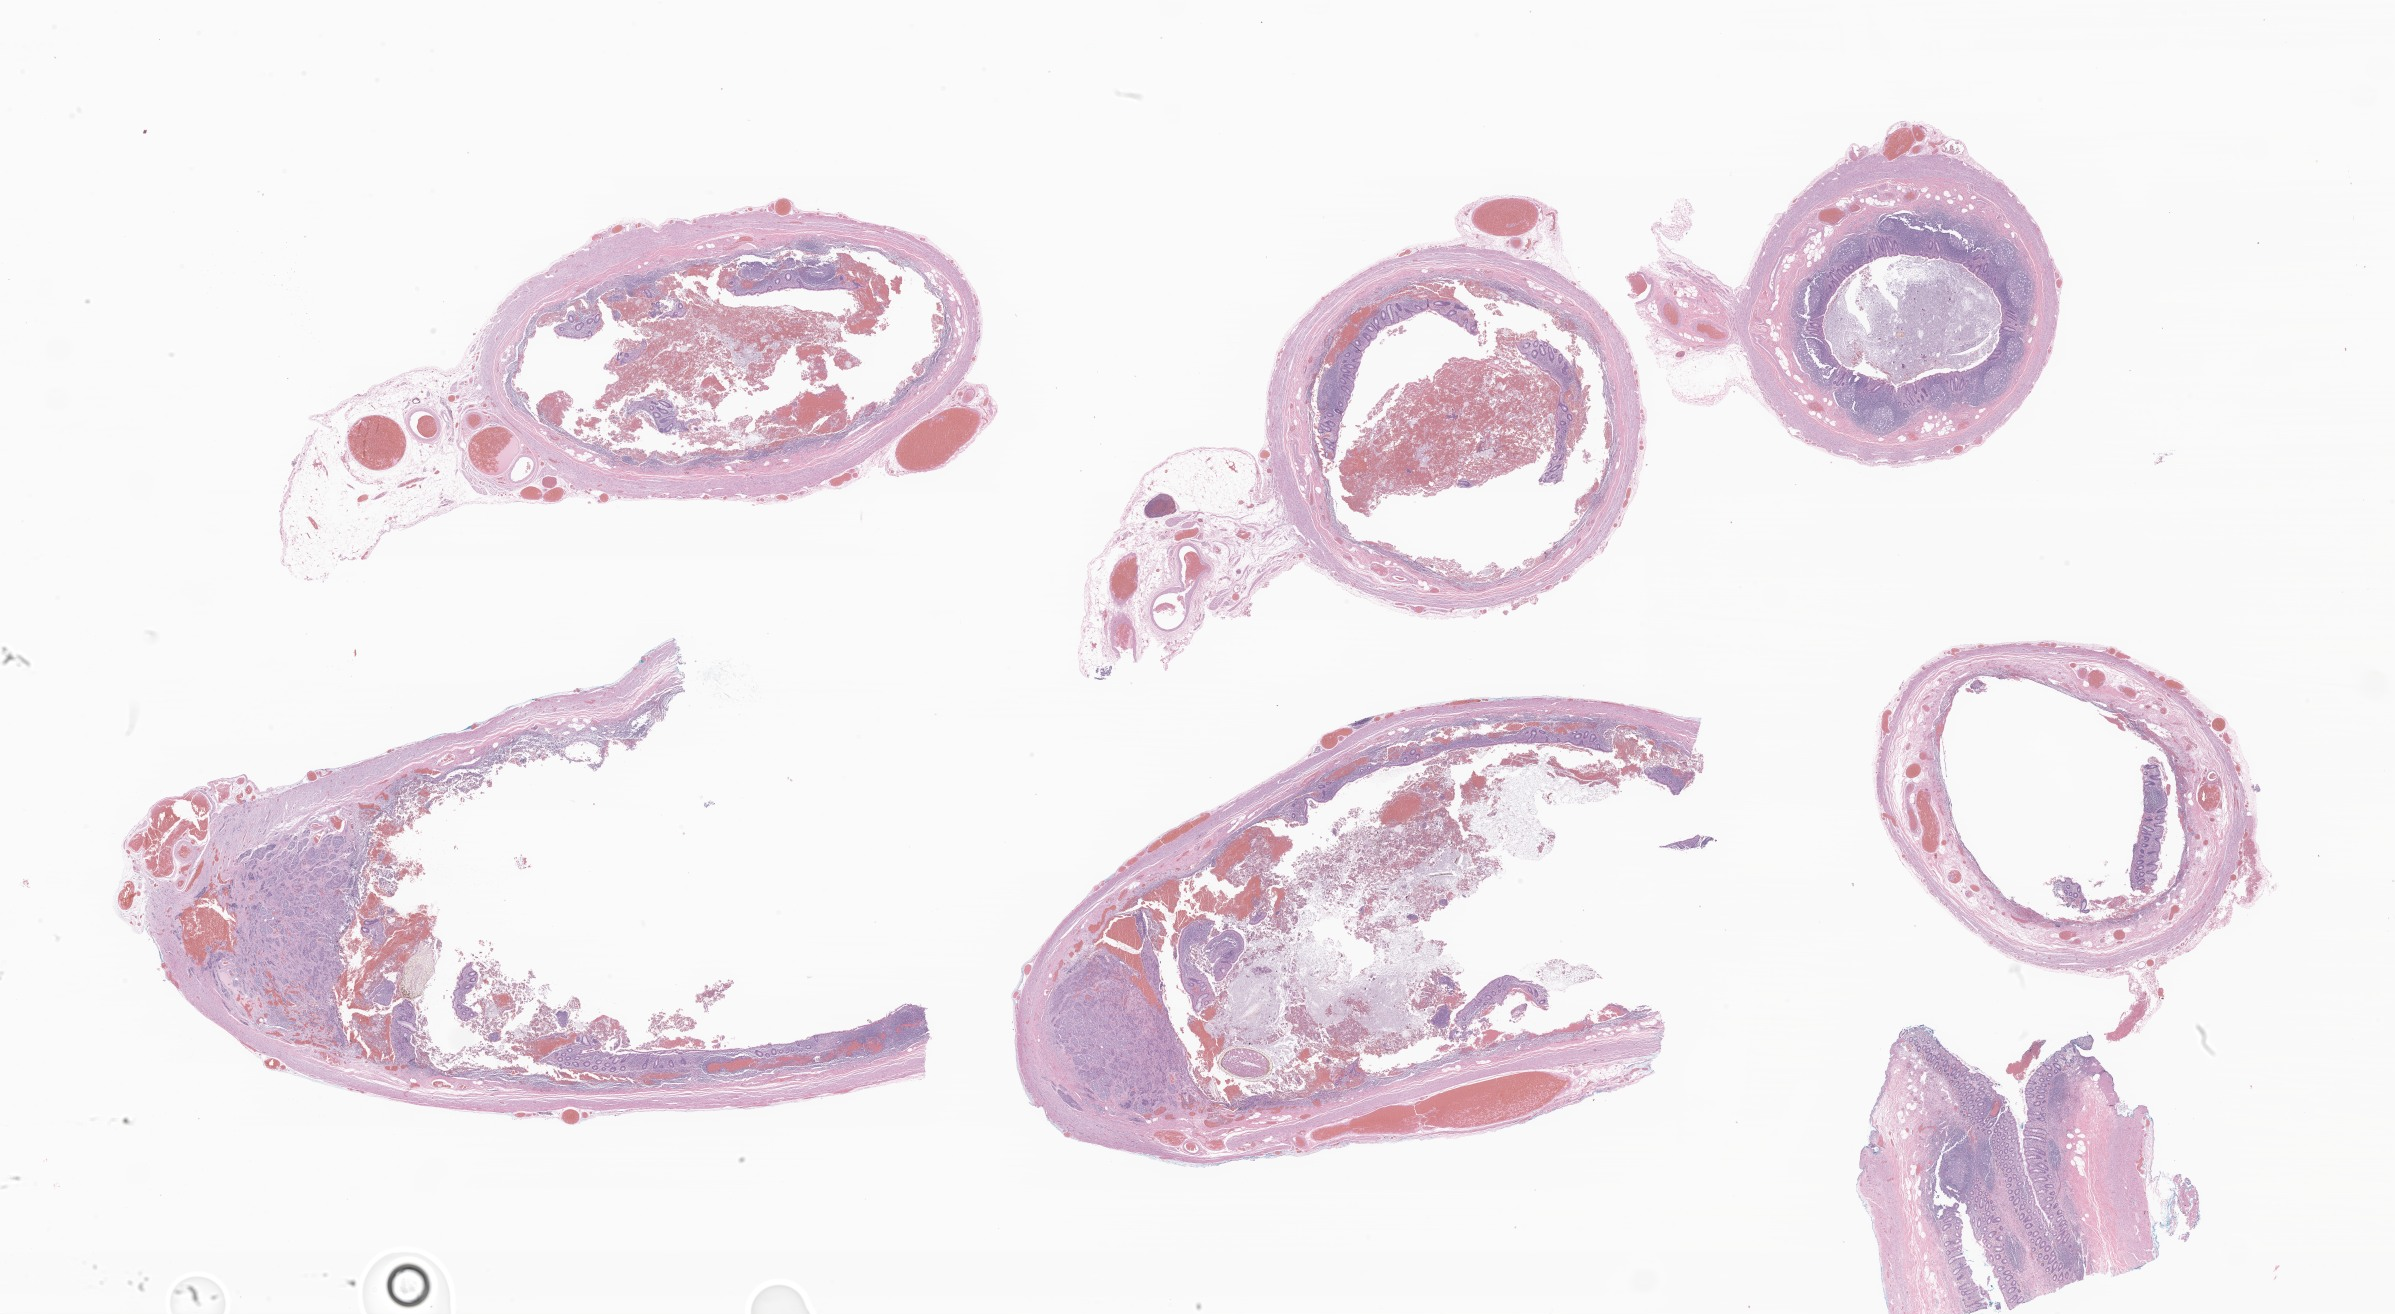
Digitized H&E-stained section of tumor tissue from the appendix, a low-resolution overview of the entire scanned area, about 40.4 x 22.2 mm. Female patient, age 211 months (17 years 7 months).
Specimen: FFPE section.